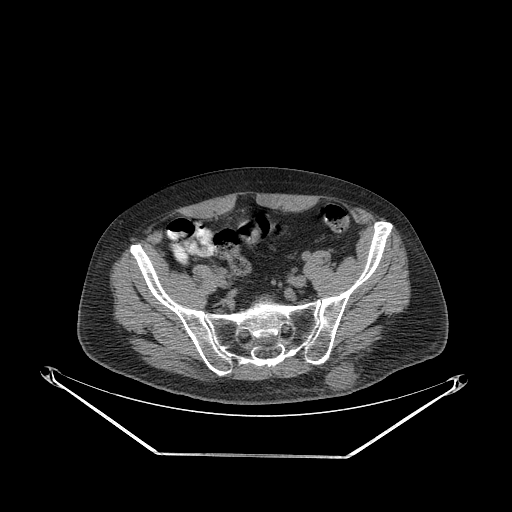
CT of an extremity soft-tissue mass (from a PET/CT study), one axial slice. Reconstruction kernel STANDARD. Soft-tissue window (W 400 / L 40 HU). 3.75 mm slice thickness. 512 × 512 image matrix, field of view 500 × 500 mm. Male patient. From the clinical record (not read from this slice): histological type: leiomyosarcoma; grade: intermediate; site of the primary tumour: left pelvis.
Outlined on this slice (expert contour drawn on MRI and transferred to this co-registered scan by the dataset authors):
- gross tumour volume (mass): bounding box (x1, y1, x2, y2) in pixels: (326, 363, 360, 391)